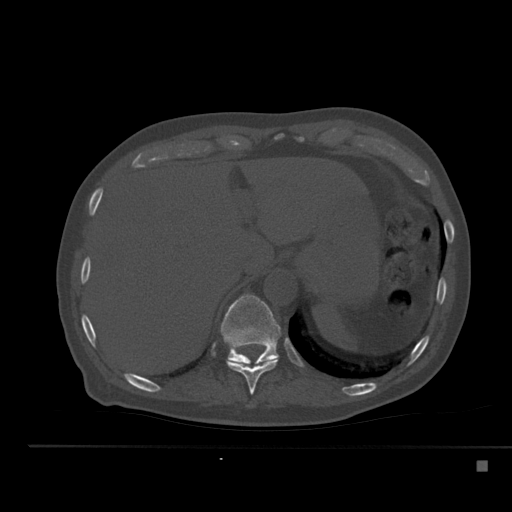
CT including the spine, one axial slice; slice 260 of 517 in the series (ordered by position); reconstruction kernel Br40s; bone window (W 1800 / L 400 HU); 512 × 512 image matrix, field of view 408 × 408 mm. Male patient, age 70 years. Case-level facts recorded for this patient, not image findings: primary cancer: renal; vertebrae with lytic lesions (as recorded): T4, T6, T10, T12, L3, L4, L5.
Annotated regions visible in this slice (semi-automatically segmented with operator editing):
- T10 vertebra: bounding box (x1, y1, x2, y2) in pixels: (226, 357, 279, 394)
- T11 vertebra: (221, 294, 280, 364)